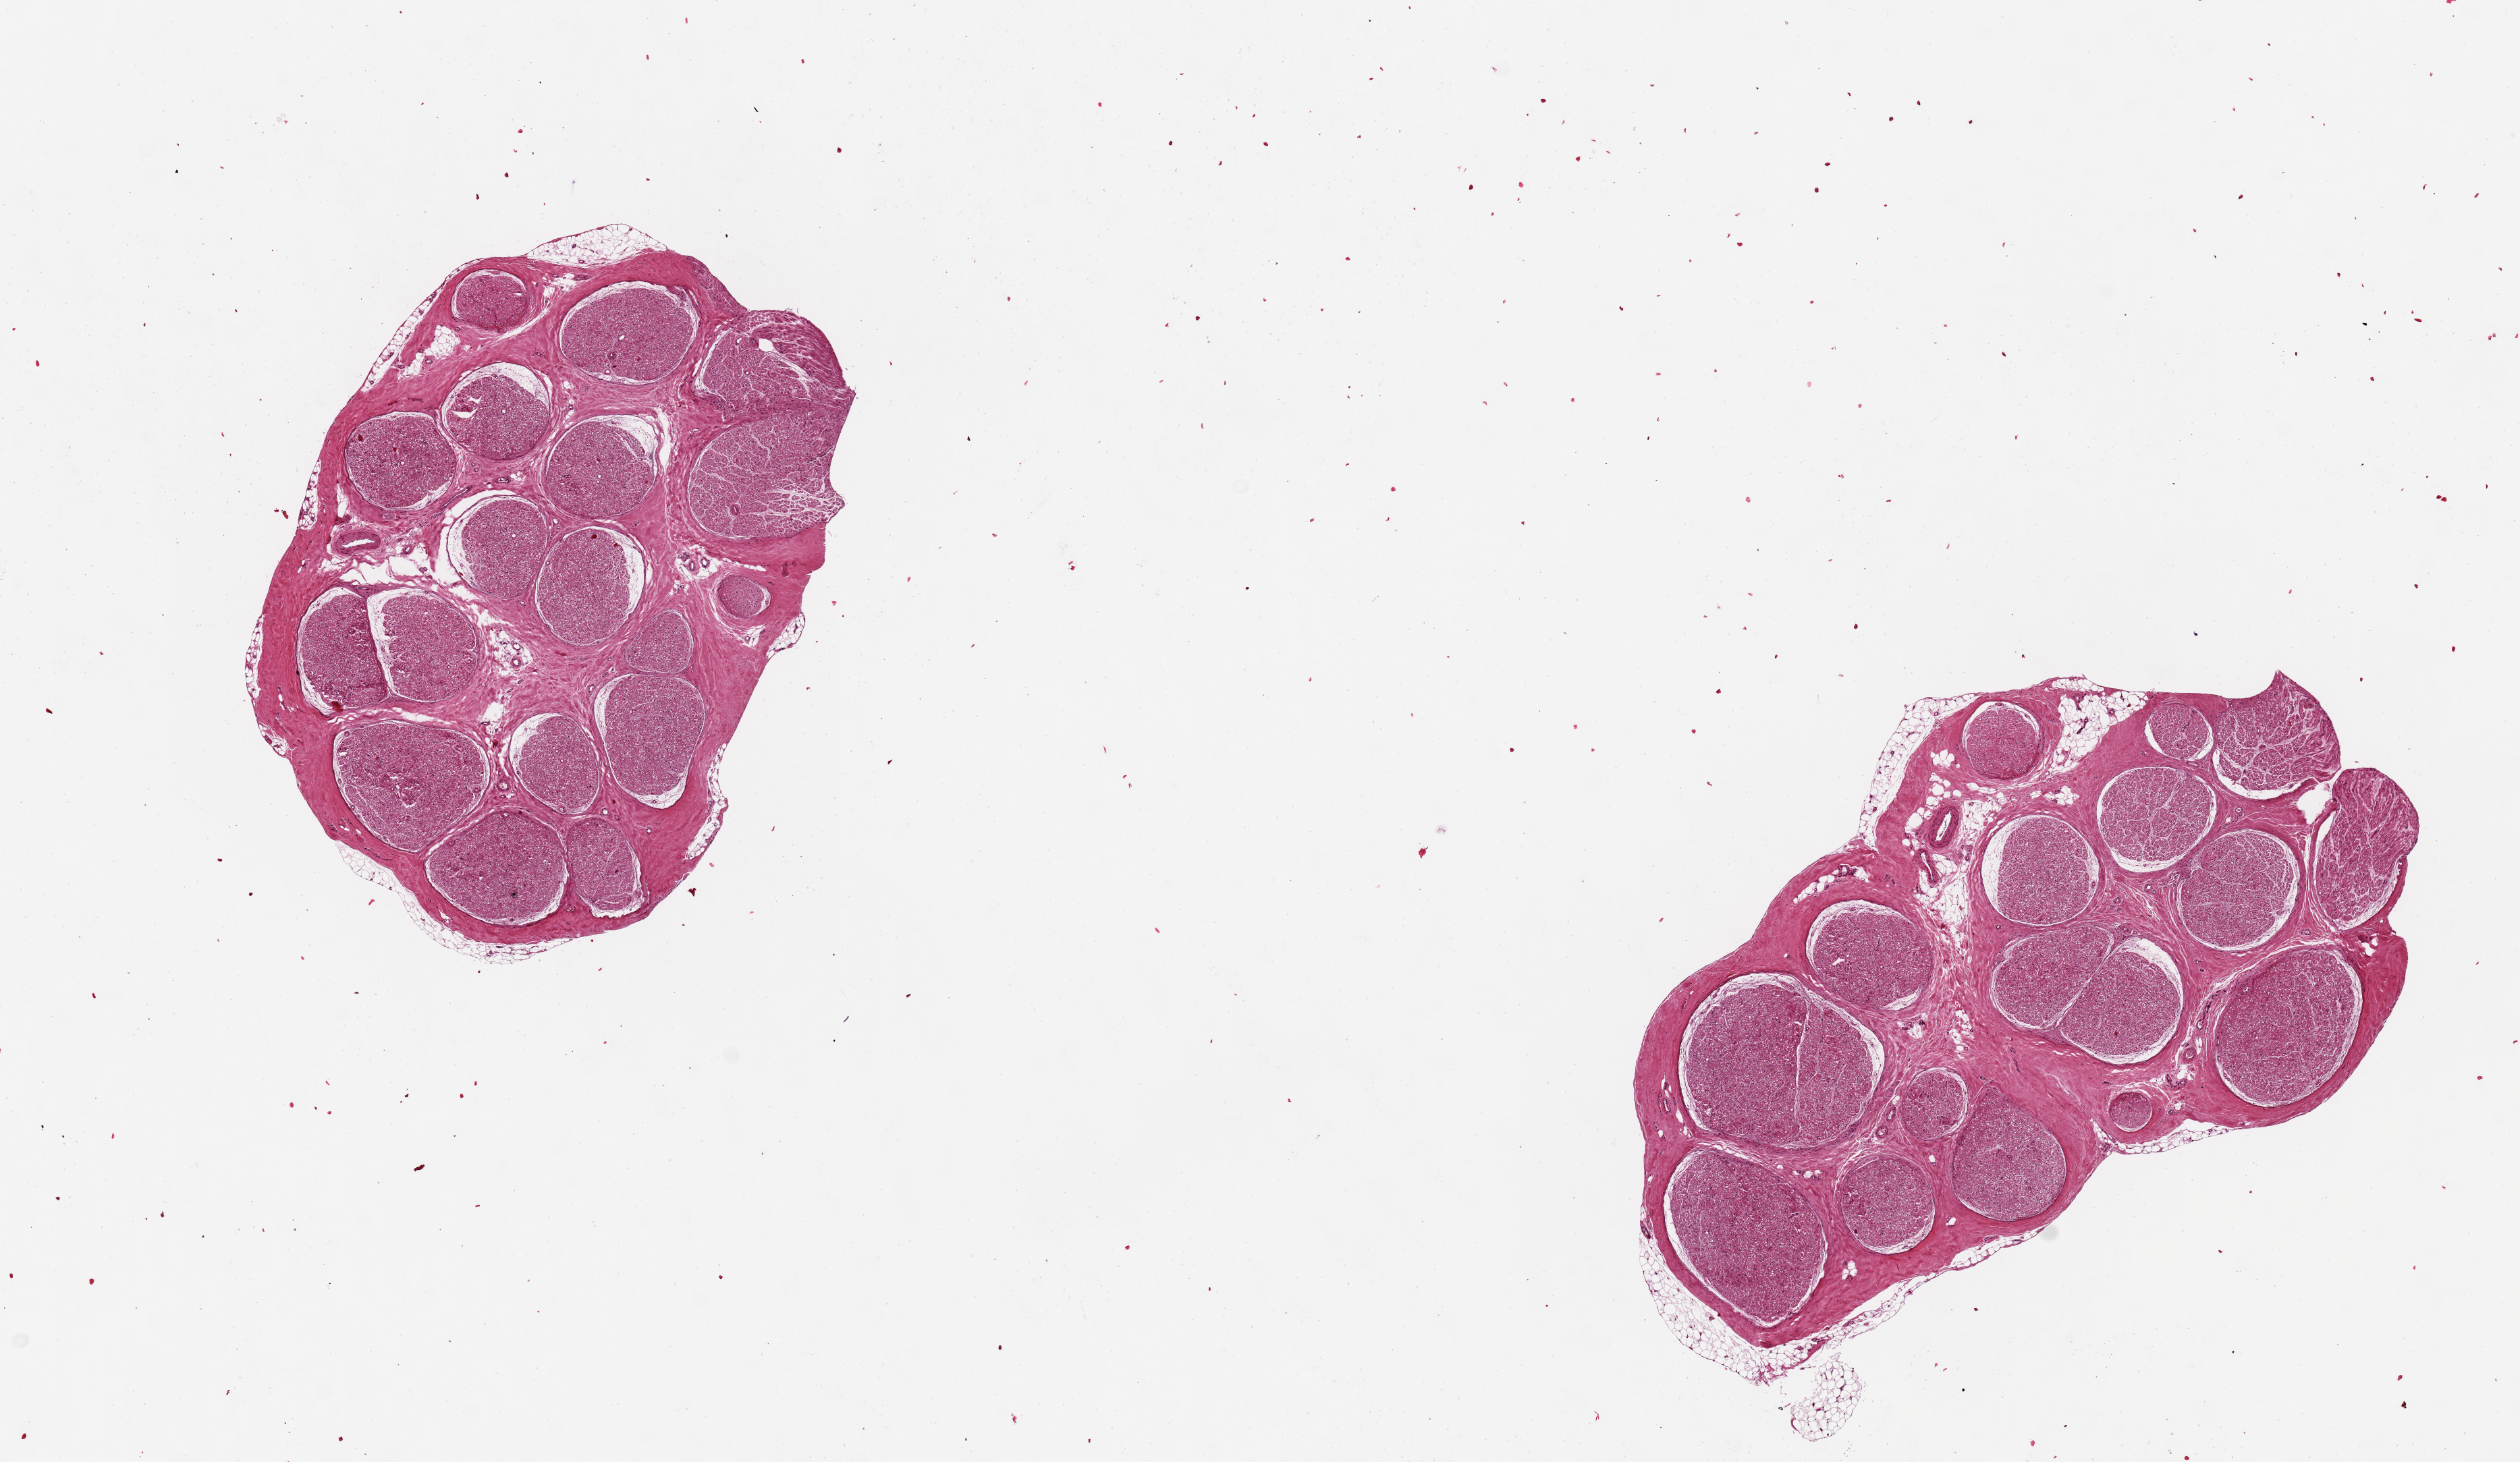
Whole-slide image, hematoxylin and eosin (H&E) stain, brightfield — shown as a low-resolution overview of the whole scanned area (about 14.8 x 8.6 mm); PAXgene-fixed, paraffin-embedded tissue; target tissue: tibial nerve; donor tissue sample. Male donor.
• review note (as recorded): 2 pieces 5x2 & 4x3 mm; virtually free of extraneous adipose